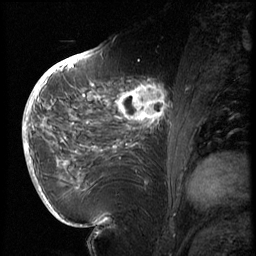
Breast MRI (dynamic contrast-enhanced), one sagittal slice; position 30 of 72 along the scan axis; 3 images stored at this slice position (order not interpretable as contrast timing); 1.5 T; TE 4.2 ms, TR 8.9 ms; 256 × 256 image matrix, field of view 200 × 200 mm. Female patient, age 56 years. From the clinical record (not read from this slice): setting: breast cancer imaged before/during neoadjuvant chemotherapy.
Outlined on this slice (semi-automatic segmentation, software-assisted and operator-edited):
- analysis volume of interest (the breast-tissue region the enhancement analysis was run in; not a lesion): bounding box (x1, y1, x2, y2) in pixels: (114, 76, 177, 138)
- tumour enhancement mask (voxels above the 140 % enhancement threshold inside the analysis volume of interest): (118, 79, 171, 124)